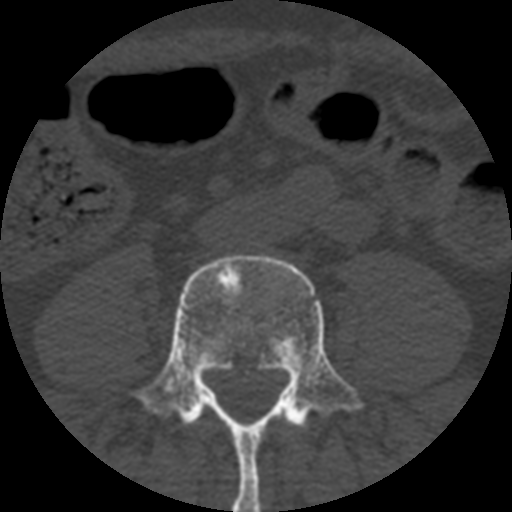
CT including the spine, one axial slice; slice 93 of 508 in the series (ordered by position); reconstruction kernel STANDARD; 120 kVp; bone window (W 1800 / L 400 HU); 1.25 mm slice thickness; 512 × 512 image matrix, field of view 160 × 160 mm. Patient age 57 years. Case-level facts recorded for this patient, not image findings: primary cancer: prostate.
Annotated regions visible in this slice (semi-automatically segmented with operator editing):
- L4 vertebra: bounding box [x1, y1, x2, y2] px = [132, 255, 364, 512]